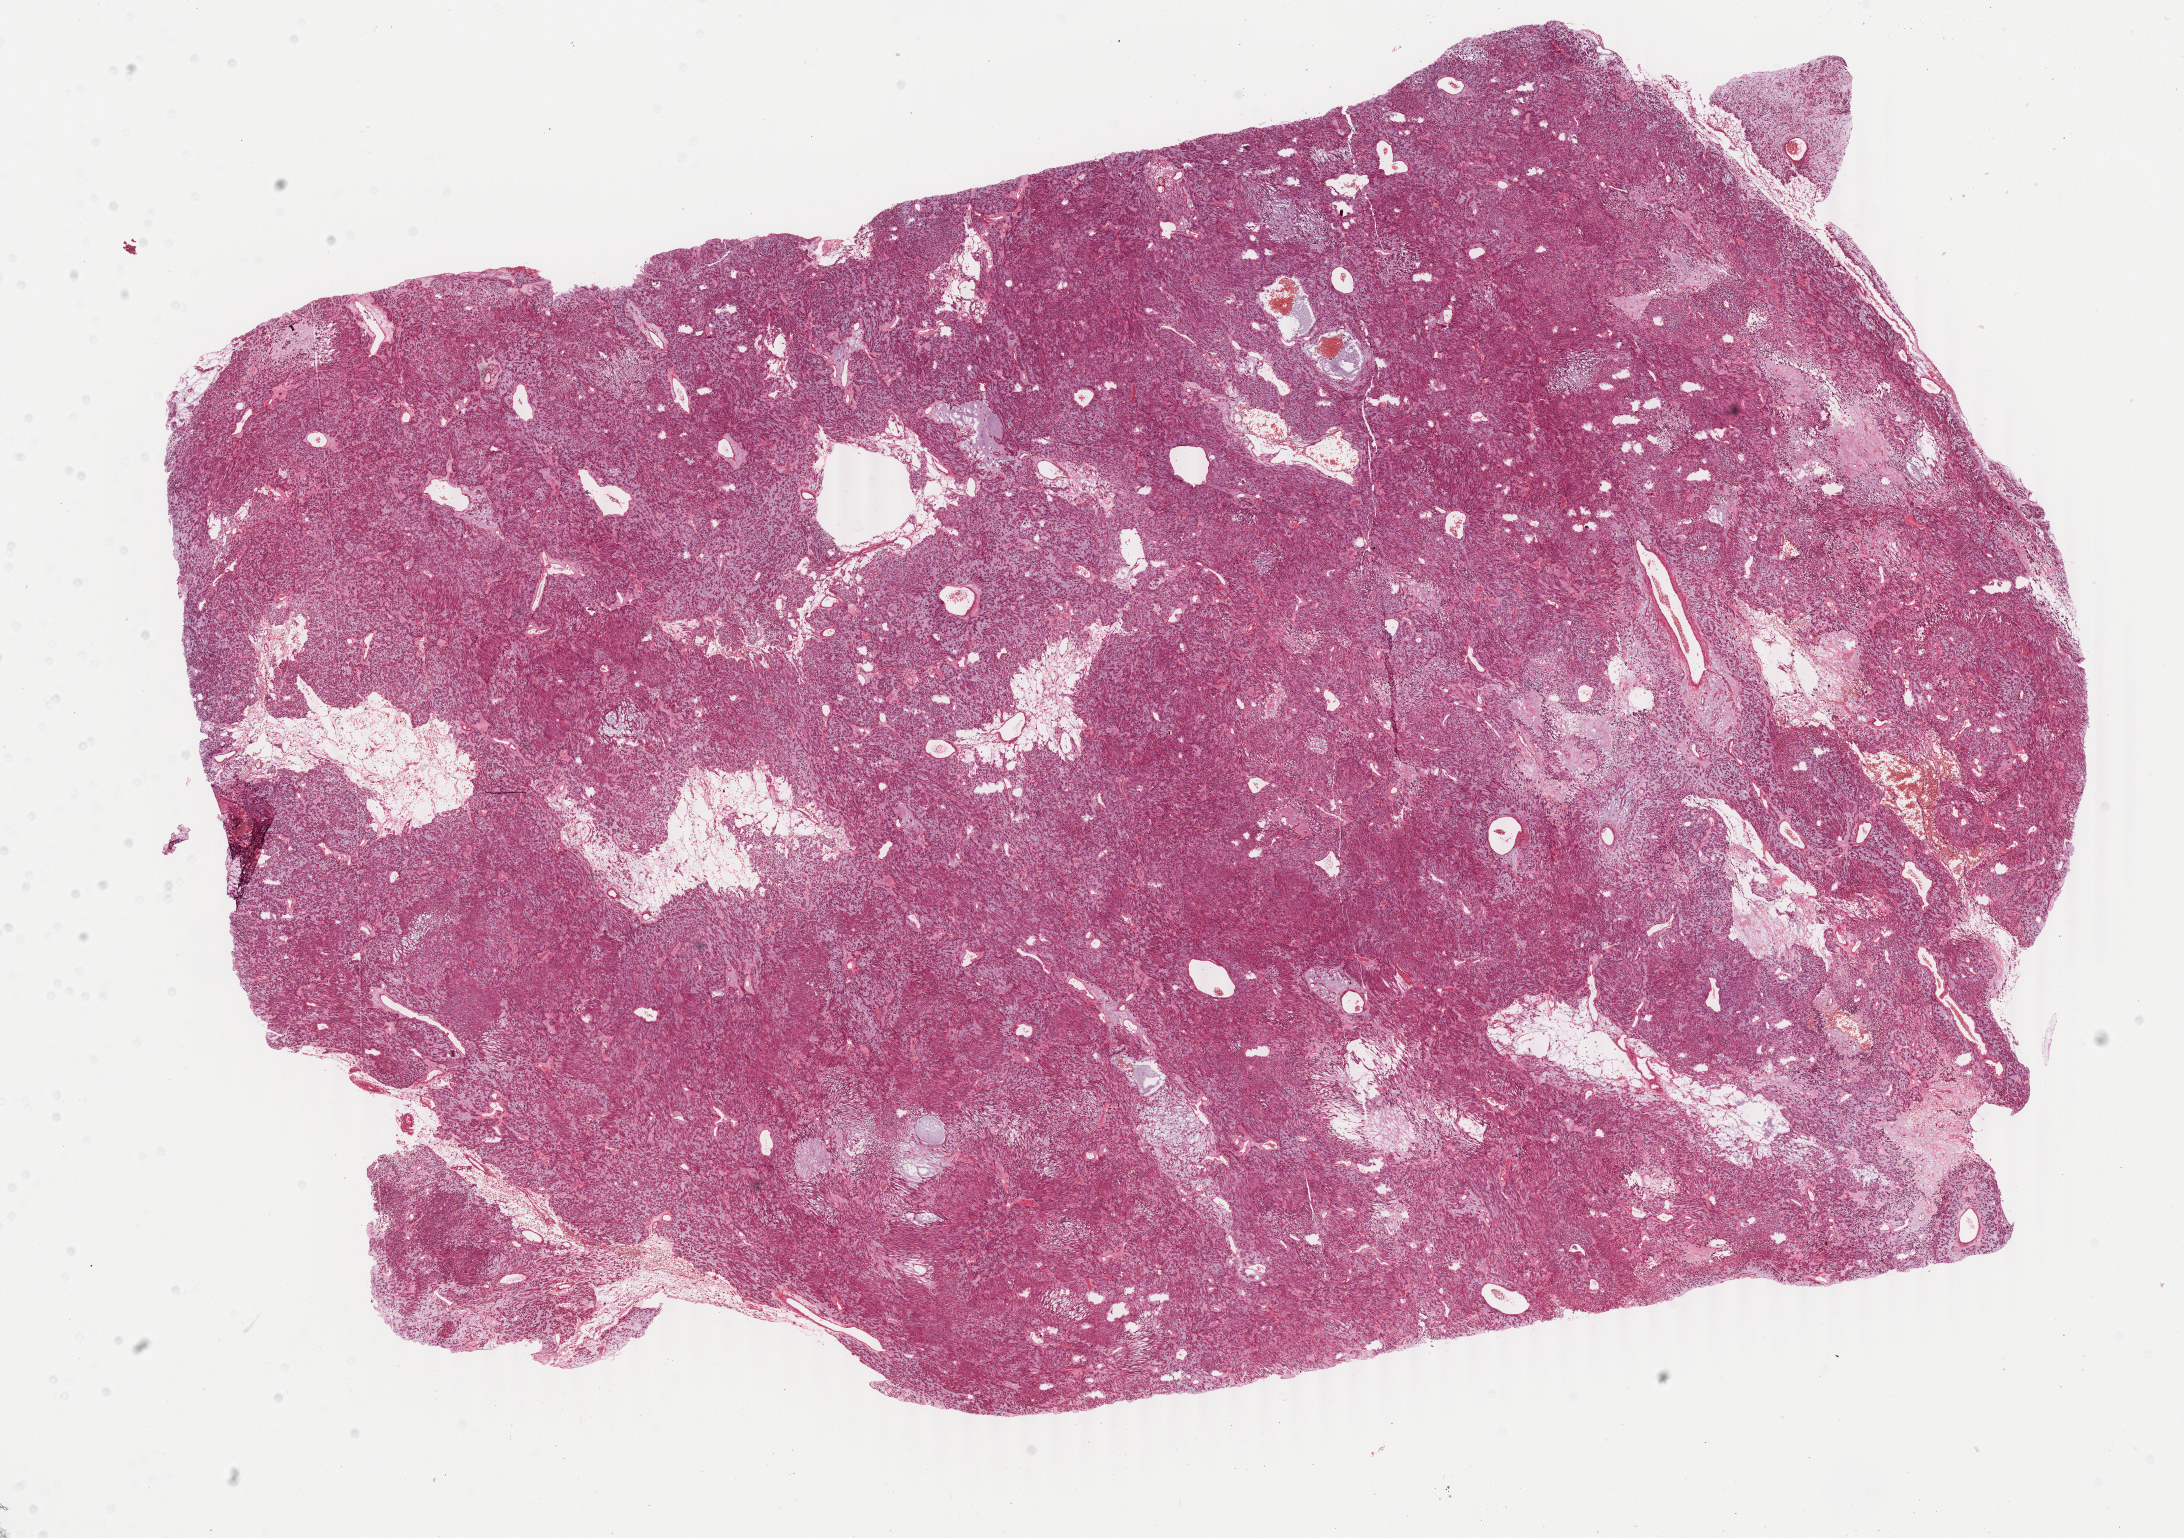
Hematoxylin and eosin (H&E) stained whole-slide image, low-resolution overview of the scanned area, about 17.4 x 12.2 mm, formalin-fixed paraffin-embedded (FFPE) diagnostic section, retroperitoneum and peritoneum, primary tumour sample. Female patient; age at initial diagnosis 75 years.
* pathologic diagnosis: Leiomyosarcoma, NOS (retroperitoneum)